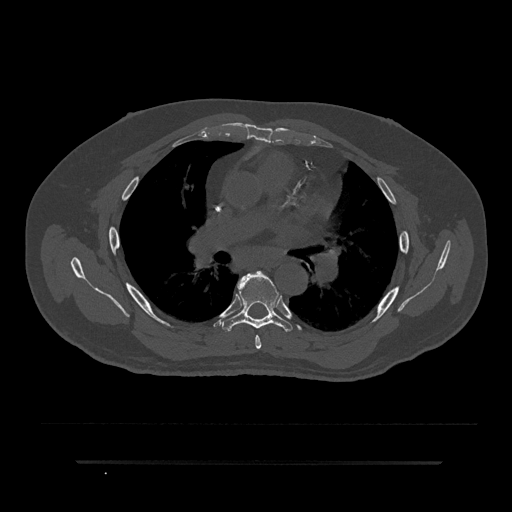
CT including the spine, one axial slice; position 537 of 797 along the scan axis; 120 kVp; bone window (W 1800 / L 400 HU); 0.5 mm slice thickness; 512 × 512 image matrix, field of view 464 × 464 mm. Patient: male, 59 years. Case-level facts recorded for this patient, not image findings: primary cancer: bile ducts; vertebrae with lytic lesions (as recorded): T10.
Structures marked on this image (semi-automatically segmented with operator editing):
- T5 vertebra: bounding box (x1, y1, x2, y2) in pixels: (255, 272, 265, 349)
- T6 vertebra: (222, 271, 292, 332)